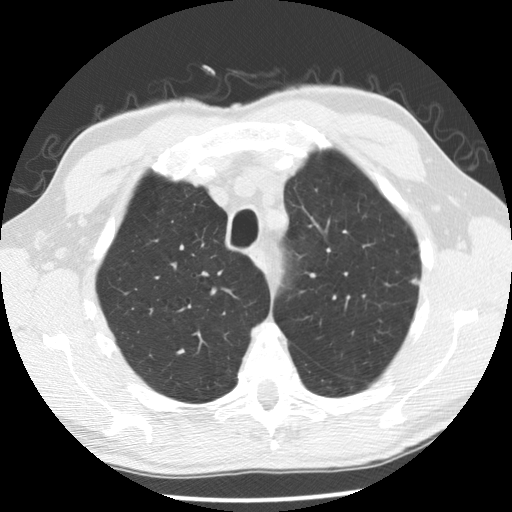
Low-dose screening chest CT, axial slice, second annual screen, lung window (W 1500 / L -600 HU), slice 34 of 173 in the series. Male participant, aged 63 years at enrolment.
Lesion marked by an expert reader, bounding box <396,264,433,297> (left, top, right, bottom; pixels). Screening reader's record for this exam (one nodule recorded; not confirmed to be the boxed lesion): non-calcified nodule or mass ≥4 mm, left upper lobe, 5 × 3 mm, poorly defined margins, soft tissue attenuation, pre-existing on the prior screen: yes; interval growth: no. Official screen result: positive, no significant change: stable abnormalities potentially related to lung cancer, unchanged since the prior screening exam. Later outcome: lung cancer diagnosed 445 days after this screen — adenocarcinoma, NOS, left upper lobe, well differentiated (G1), stage IB (AJCC 6th edition), 5 mm at pathology.